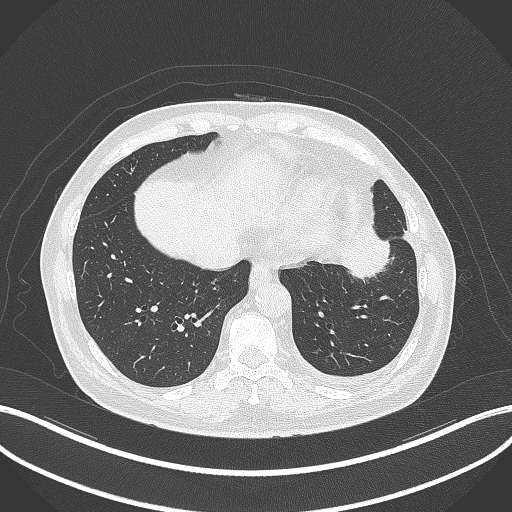
Chest CT, one axial slice; slice 93 of 230 in the series (ordered by position); reconstruction kernel B70f; lung window (W 1500 / L -600 HU); 1 mm slice thickness; 512 × 512 image matrix, field of view 400 × 400 mm. Patient: male, 68 years. From the clinical record (not read from this slice): clinical TNM (as recorded): T2b N0 M0.
Structures marked on this image (bounding box drawn by a radiologist):
- lung tumour (recorded histology: squamous cell carcinoma): box from (x=340, y=218) to (x=397, y=283) px